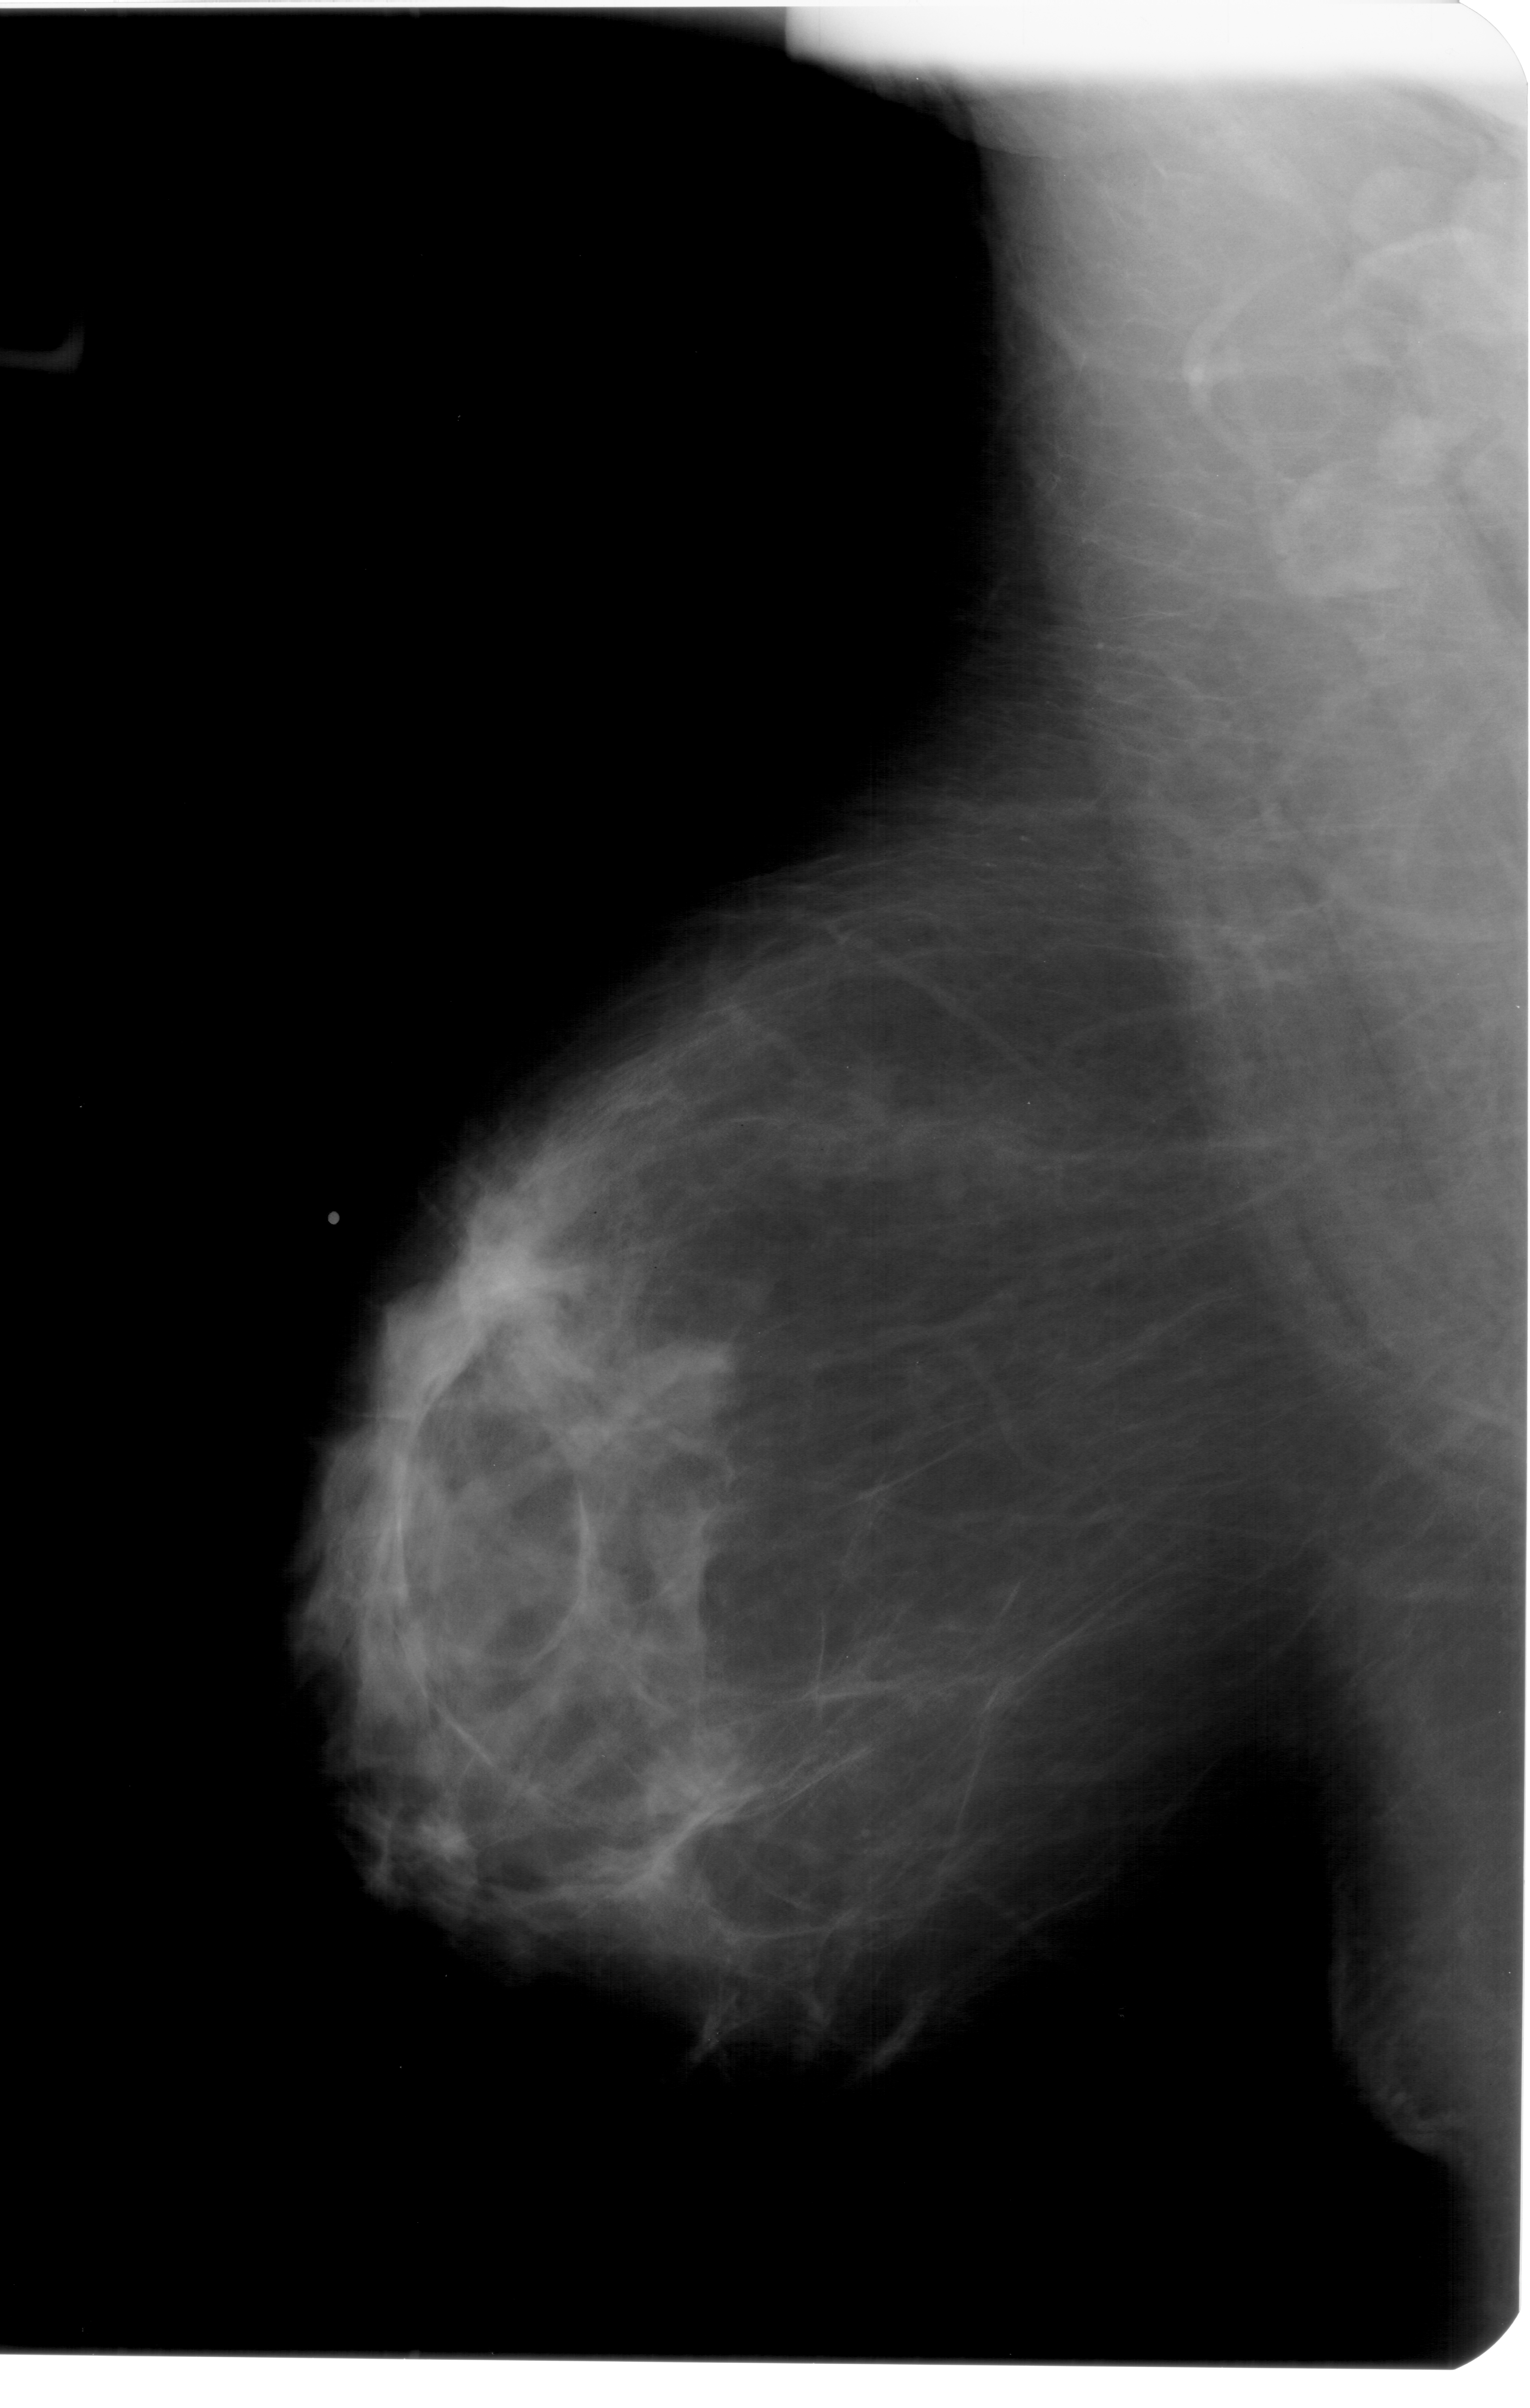
Scanned film-screen mammogram. Left breast. MLO view. 1530 × 2408 image matrix.
Expert-marked regions of interest on this film, with their recorded descriptors:
- mass, shape irregular, margins spiculated; BI-RADS assessment category 5; subtlety rating 2 on a 1 (subtle) to 5 (obvious) scale; pathology result (as recorded, not read from the image): malignant: bounding box (x1, y1, x2, y2) in pixels: (426, 1226, 586, 1380)